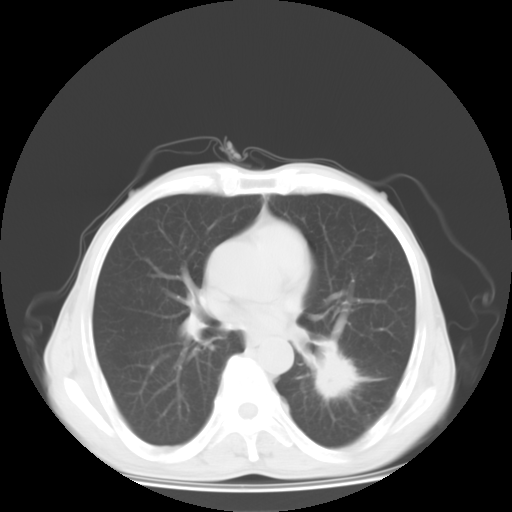
Chest CT, one axial slice. Position 11 of 27 along the scan axis. Reconstruction kernel STANDARD. 120 kVp. Lung window (W 1500 / L -600 HU). 10 mm slice thickness. 512 × 512 image matrix. Male patient, age 63 years. Case-level facts recorded for this patient, not image findings: clinical TNM (as recorded): T1c N0 M1b.
Structures marked on this image (bounding box drawn by a radiologist):
- lung tumour (recorded histology: adenocarcinoma): box from (x=308, y=339) to (x=389, y=404) px